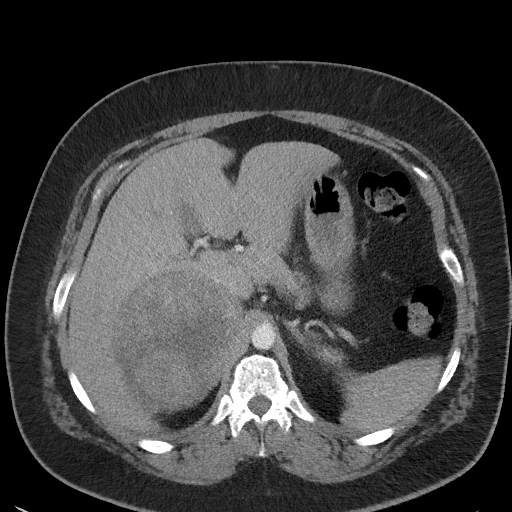
Contrast-enhanced abdominal CT, one axial slice; position 35 of 56 along the scan axis; reconstruction kernel I41f/3; 120 kVp; intravenous contrast given; soft-tissue window (W 400 / L 40 HU); 512 × 512 image matrix, field of view 373 × 373 mm. Female patient, age 35 years. From the clinical record (not read from this slice): diagnosis: adrenocortical carcinoma; tumour side: right adrenal; tumour size at pathology: 15 cm; Ki-67 index: 40 %; stage (as recorded): 2.
Annotated regions visible in this slice (semi-automatically segmented with operator editing):
- mass: box from (x=117, y=272) to (x=243, y=409) px